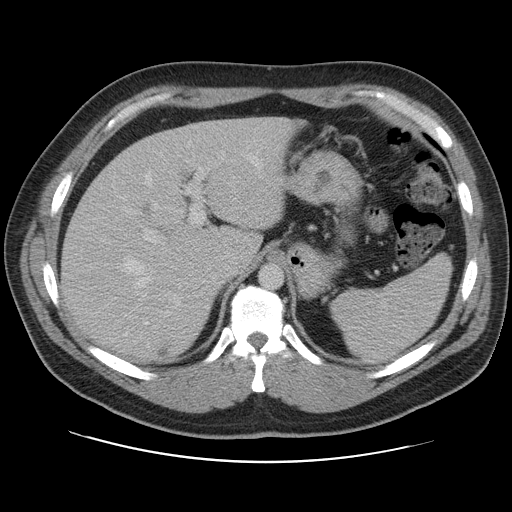
Contrast-enhanced abdominal CT, one axial slice; slice 79 of 109 in the series (ordered by position); 120 kVp; intravenous contrast given; soft-tissue window (W 400 / L 40 HU); 512 × 512 image matrix, field of view 402 × 402 mm. Male patient, age 35 years. Case-level facts recorded for this patient, not image findings: diagnosis: colorectal cancer liver metastases, imaged before liver resection; multiple liver metastases: yes; largest metastasis: 2.8 cm; disease in both lobes: yes.
Annotated regions visible in this slice (outlined manually by an expert reader):
- hepatic veins: bounding box (x1, y1, x2, y2) in pixels: (118, 152, 262, 325)
- liver: (62, 118, 294, 360)
- planned liver remnant (the part of the liver to remain after resection): (62, 118, 287, 357)
- portal vein (with intrahepatic branches): (100, 160, 216, 301)
- liver metastasis: (158, 349, 170, 358)